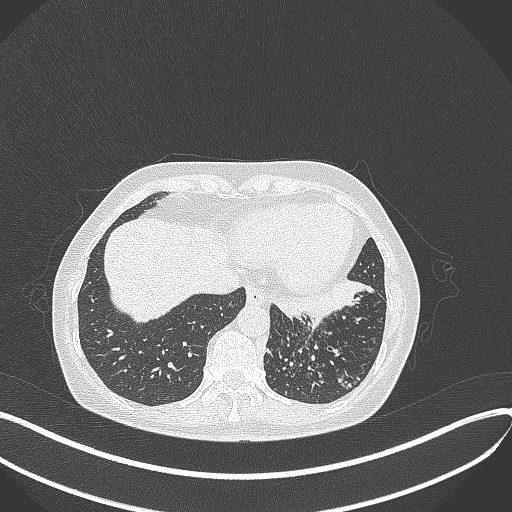
Chest CT, one axial slice; slice 103 of 429 in the series (ordered by position); reconstruction kernel B70f; 100 kVp; lung window (W 1500 / L -600 HU); 512 × 512 image matrix, field of view 400 × 400 mm. Patient: female, 63 years. Case-level facts recorded for this patient, not image findings: clinical TNM (as recorded): T1b N0 M0; histopathological grade: G2-3.
Structures marked on this image (bounding box drawn by a radiologist):
- lung tumour (recorded histology: adenocarcinoma): bounding box <270,278,377,325> (left, top, right, bottom; pixels)